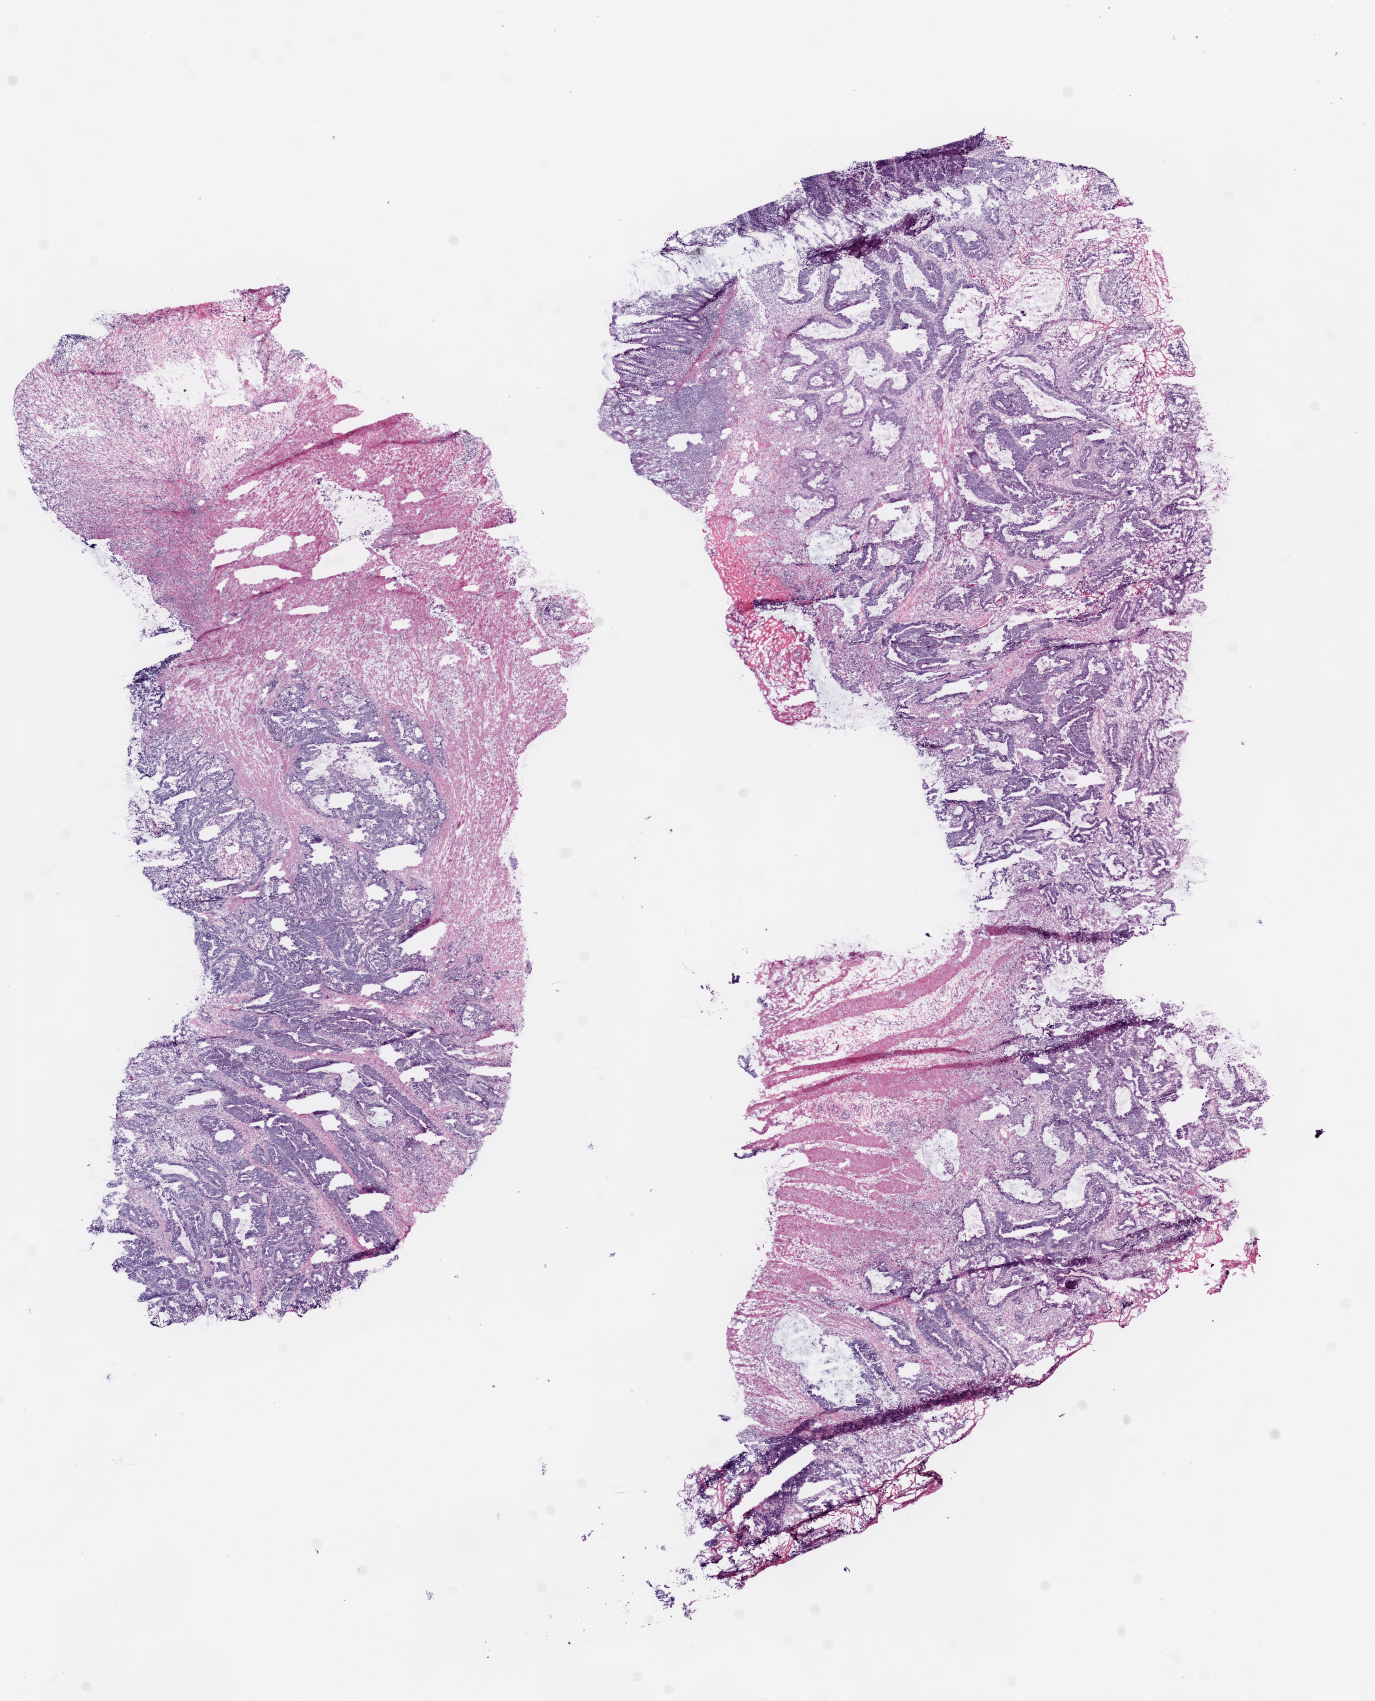
Whole-slide histology image, H&E-stained, whole scanned area (about 11.0 x 13.6 mm, slide scanned at 20x) shown as a low-resolution overview. Frozen section from the bottom of the tissue portion. Colon, primary tumour sample. Female patient; age at initial diagnosis 73 years. Slide review estimates, as recorded: tumour cells 73%, tumour nuclei 70%, normal cells 10%, stromal cells 10%, necrosis 7%.
• AJCC pathologic stage: IIA
• lymph nodes positive (case pathology): 0 of 23 examined
• pathologic diagnosis: Adenocarcinoma, NOS